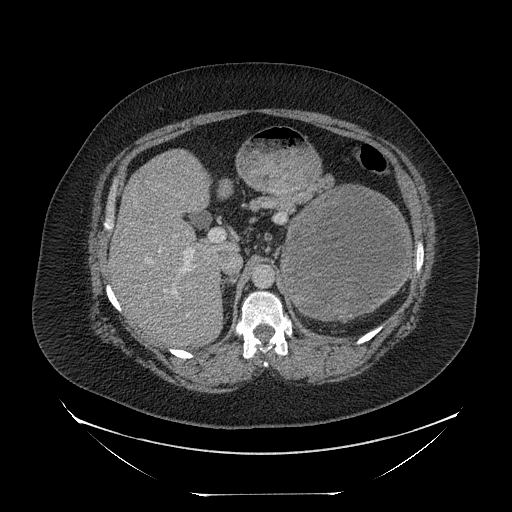
Contrast-enhanced abdominal CT, one axial slice; position 150 of 205 along the scan axis; 120 kVp; intravenous contrast given; soft-tissue window (W 400 / L 40 HU); 2.5 mm slice thickness; 512 × 512 image matrix, field of view 500 × 500 mm. Patient: female, 53 years. Case-level facts recorded for this patient, not image findings: diagnosis: adrenocortical carcinoma; tumour side: left adrenal; tumour size at pathology: 17 cm; Ki-67 index: 20 %; stage (as recorded): 3.
Outlined on this slice (semi-automatic segmentation, software-assisted and operator-edited):
- mass: bounding box [x1, y1, x2, y2] px = [284, 187, 410, 319]